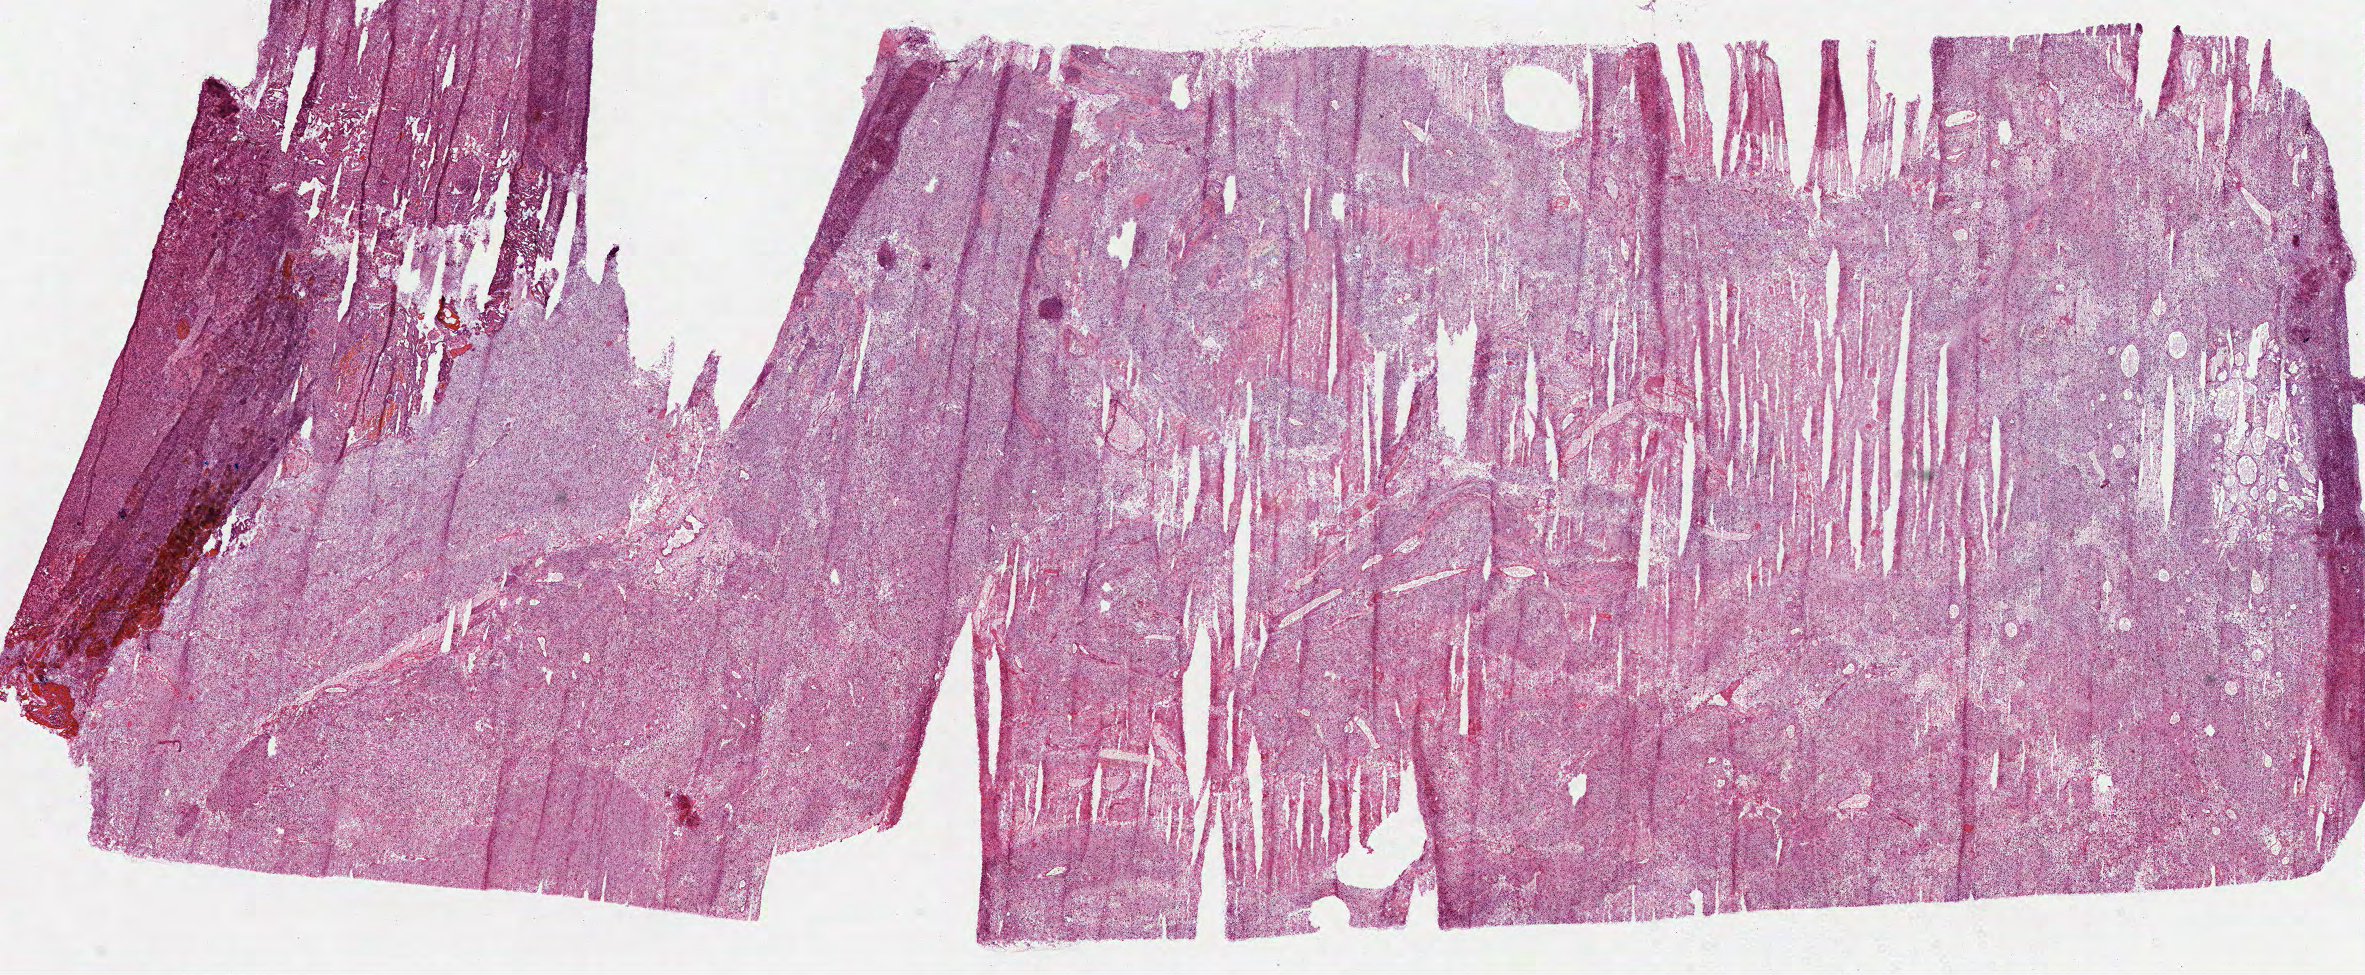
Whole-slide histology image, H&E-stained — a low-resolution overview of the entire scanned area, about 19.1 x 7.9 mm (acquisition: 40x scan), frozen section from the top of the tissue portion, primary tumour sample from the brain. Patient: female, age at initial diagnosis 73 years. Composition of this section per pathologist review: tumour cells 90%, tumour nuclei 85%, normal cells 0%, stromal cells 0%, necrosis 10%.
Diagnosis: Glioblastoma.